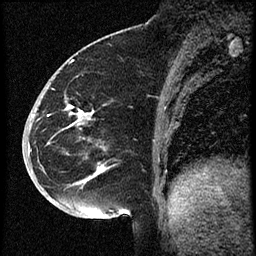
Breast MRI (dynamic contrast-enhanced), one sagittal slice; slice 23 of 60 in the series (ordered by position); dynamic contrast-enhanced study with each time point stored as its own series, time point 2 of 3 at this slice position (early post-contrast, ordered by acquisition time); 1.5 T; TE 4.2 ms, TR 18.9 ms; 256 × 256 image matrix, field of view 200 × 200 mm. Female patient. Case-level facts recorded for this patient, not image findings: setting: breast cancer imaged before/during neoadjuvant chemotherapy; receptor status: HR-positive, HER2-negative.
Annotated regions visible in this slice (semi-automatic segmentation, software-assisted and operator-edited):
- analysis volume of interest (the breast-tissue region the enhancement analysis was run in; not a lesion): box from (x=30, y=87) to (x=114, y=173) px
- tumour enhancement mask (voxels above the 100 % enhancement threshold inside the analysis volume of interest): (x=68, y=105)–(x=86, y=116)